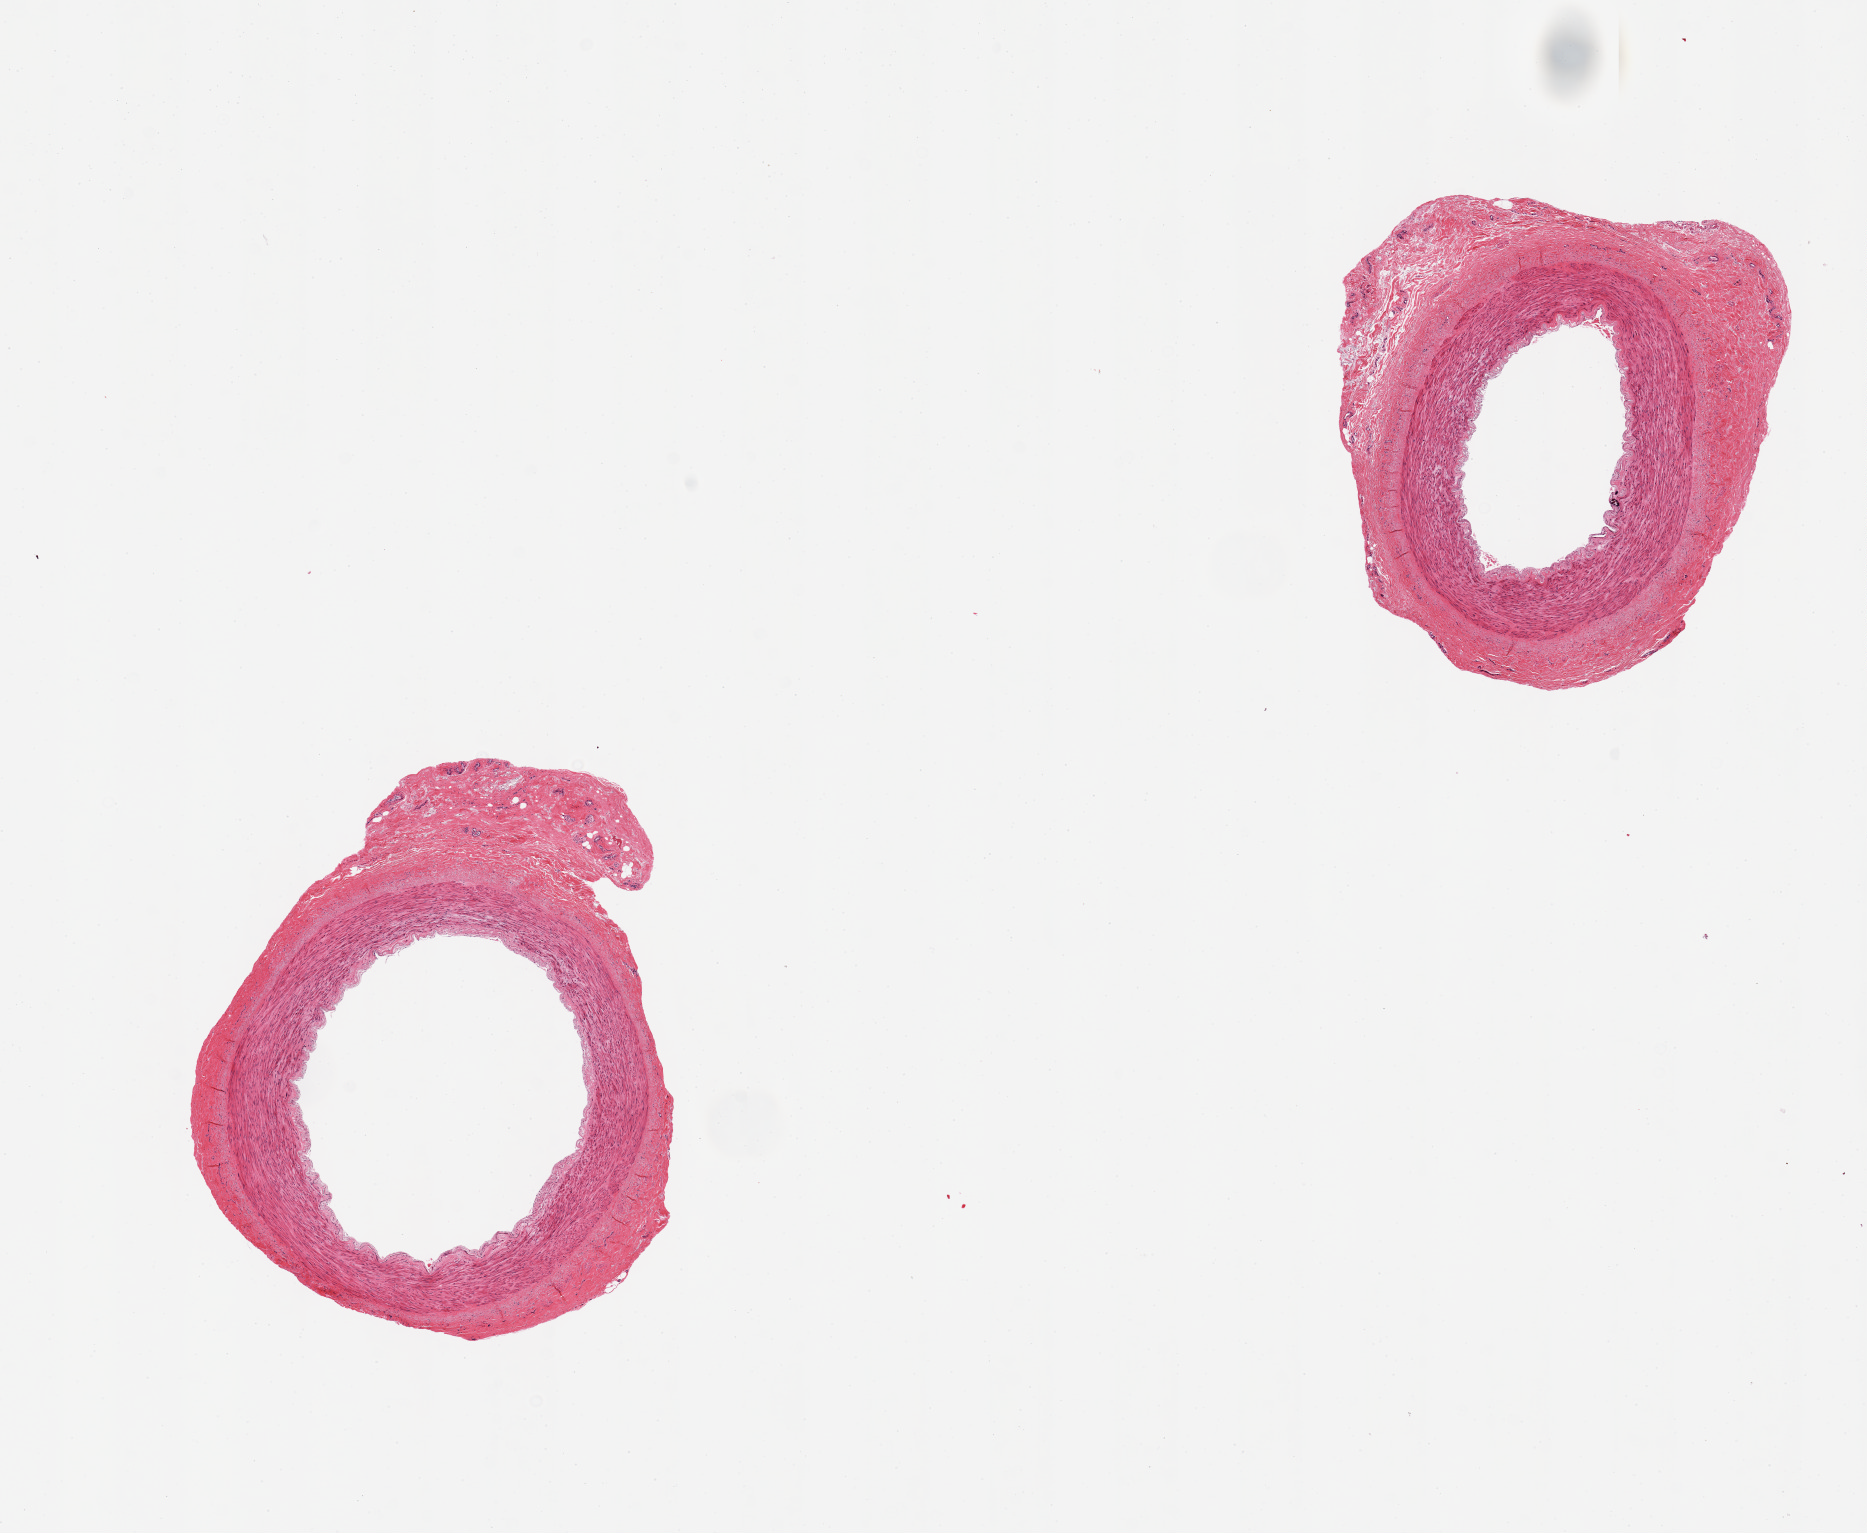
H&E whole-slide image, shown as a low-resolution overview of the whole scanned area (about 14.8 x 12.1 mm, from a 20x scan); PAXgene-fixed, paraffin-embedded tissue; target tissue: tibial artery; tissue donor sample. Donor: female.
• review note (as recorded): 2 pieces; well trimmed of fat; some perivascular stroma present